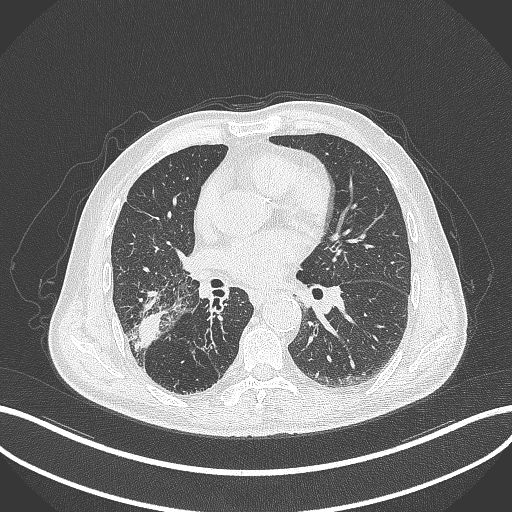
Chest CT, one axial slice. Slice 207 of 429 in the series (ordered by position). Reconstruction kernel B70f. Lung window (W 1500 / L -600 HU). 1 mm slice thickness. 512 × 512 image matrix, field of view 400 × 400 mm. Male patient, age 72 years. From the clinical record (not read from this slice): clinical TNM (as recorded): T3 N2 M0.
Annotated regions visible in this slice (bounding box drawn by a radiologist):
- lung tumour (recorded histology: adenocarcinoma): bounding box (x1, y1, x2, y2) in pixels: (129, 305, 172, 354)